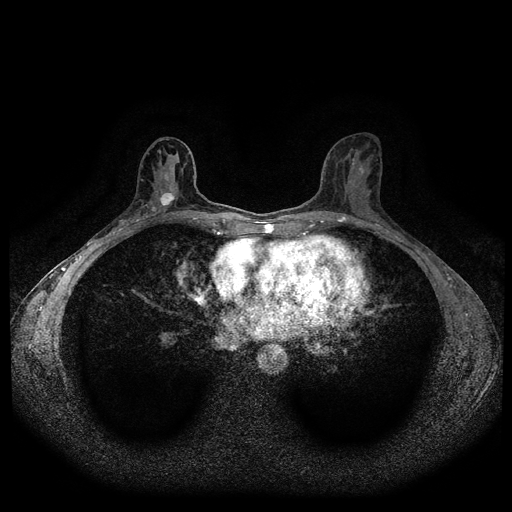
Breast MRI (dynamic contrast-enhanced, multi-phase), one axial slice. Position 54 of 116 along the scan axis. Dynamic contrast-enhanced series, time point 2 of 5 at this slice position (early post-contrast). 1.5 T. TE 2.6 ms, TR 5.3 ms. 2 mm slice thickness. 512 × 512 image matrix, field of view 350 × 350 mm. Female patient, age 50 years.
Structures marked on this image (semi-automatically segmented with operator editing):
- breast lesion (labelled 'tumour' in the annotation; benign lesions carry a separate 'benign' label): bounding box [x1, y1, x2, y2] px = [151, 189, 175, 212]